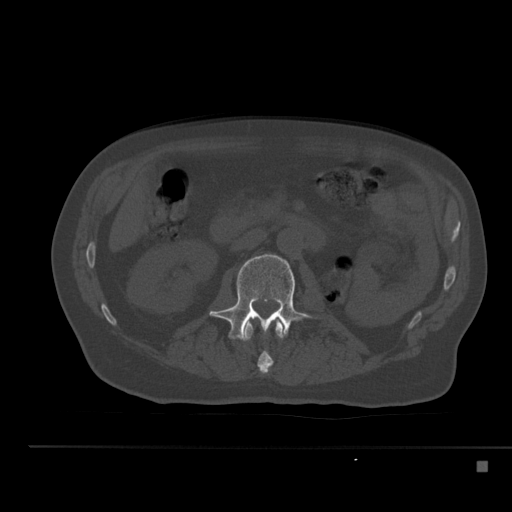
CT including the spine, one axial slice; position 189 of 517 along the scan axis; reconstruction kernel Br40s; 120 kVp; bone window (W 1800 / L 400 HU); 1.5 mm slice thickness; 512 × 512 image matrix, field of view 408 × 408 mm. Male patient, age 70 years. From the clinical record (not read from this slice): primary cancer: renal; vertebrae with lytic lesions (as recorded): T4, T6, T10, T12, L3, L4, L5.
Annotated regions visible in this slice (semi-automatically segmented with operator editing):
- L1 vertebra: bounding box <240,319,286,374> (left, top, right, bottom; pixels)
- L2 vertebra: <209,254,313,339>